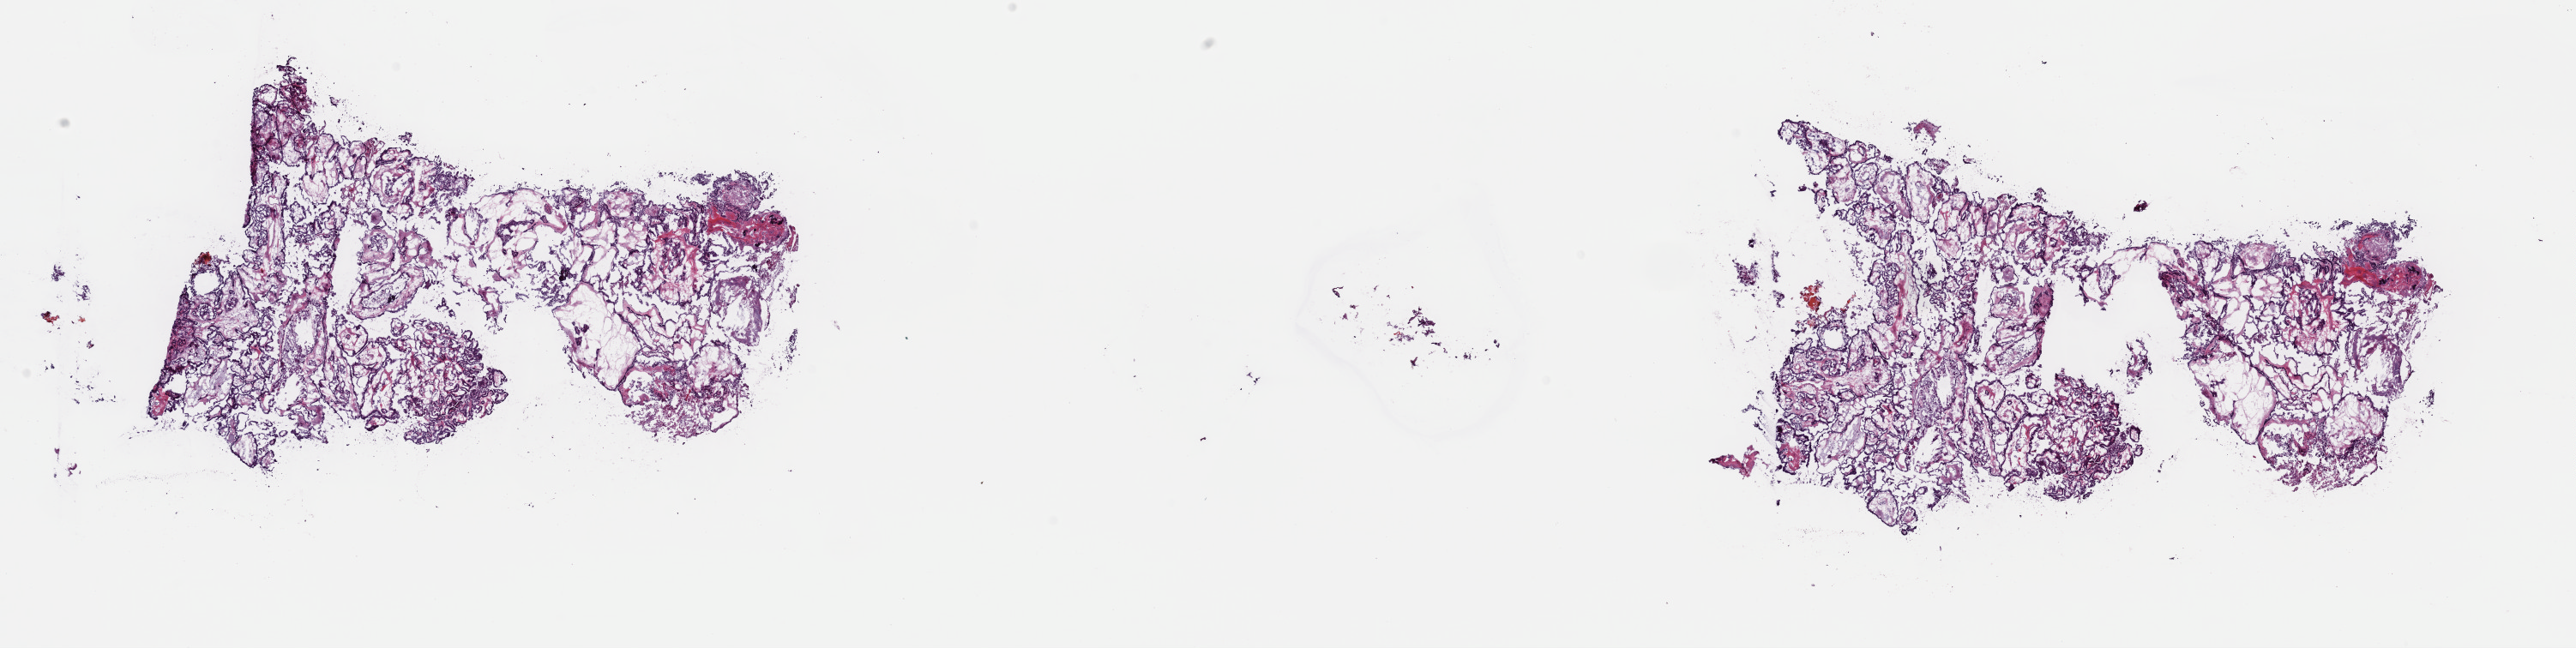
Digitized H&E tissue section (whole slide), shown as a low-resolution overview of the whole scanned area (about 23.7 x 6.0 mm, from a 40x scan). Frozen section from the top of the tissue portion. Sample: primary tumour, thyroid. Female patient; age at initial diagnosis 41 years. Composition of this section per pathologist review: tumour cells 85%, tumour nuclei 85%, normal cells 0%, stromal cells 15%, necrosis 0%. Infiltration values recorded for this section: lymphocyte infiltration 2%, monocyte infiltration 0%, neutrophil infiltration 0%.
AJCC pathologic stage: I (5th edition). Diagnosis: Papillary adenocarcinoma, NOS (thyroid gland). Laterality: right. Lymph nodes positive (case pathology): 3 of 40 examined.